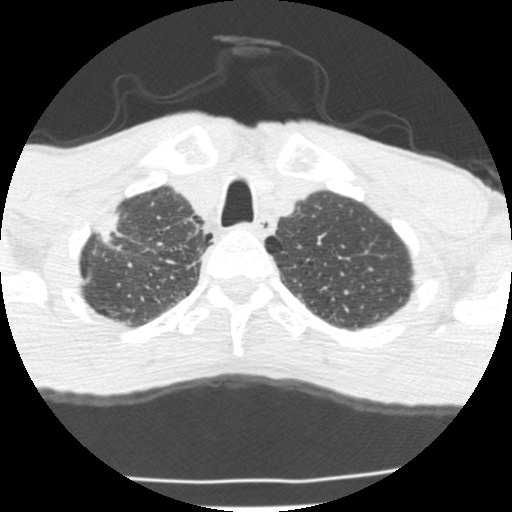
Low-dose screening chest CT, one axial slice; position 185 of 214 along the scan axis; reconstruction kernel STANDARD; 120 kVp; lung window (W 1500 / L -600 HU); 512 × 512 image matrix, field of view 283 × 283 mm.
Annotated regions visible in this slice (manually delineated by an expert):
- lesion 1 (tumor, upper lobe of right lung): bounding box (x1, y1, x2, y2) in pixels: (97, 214, 120, 247)